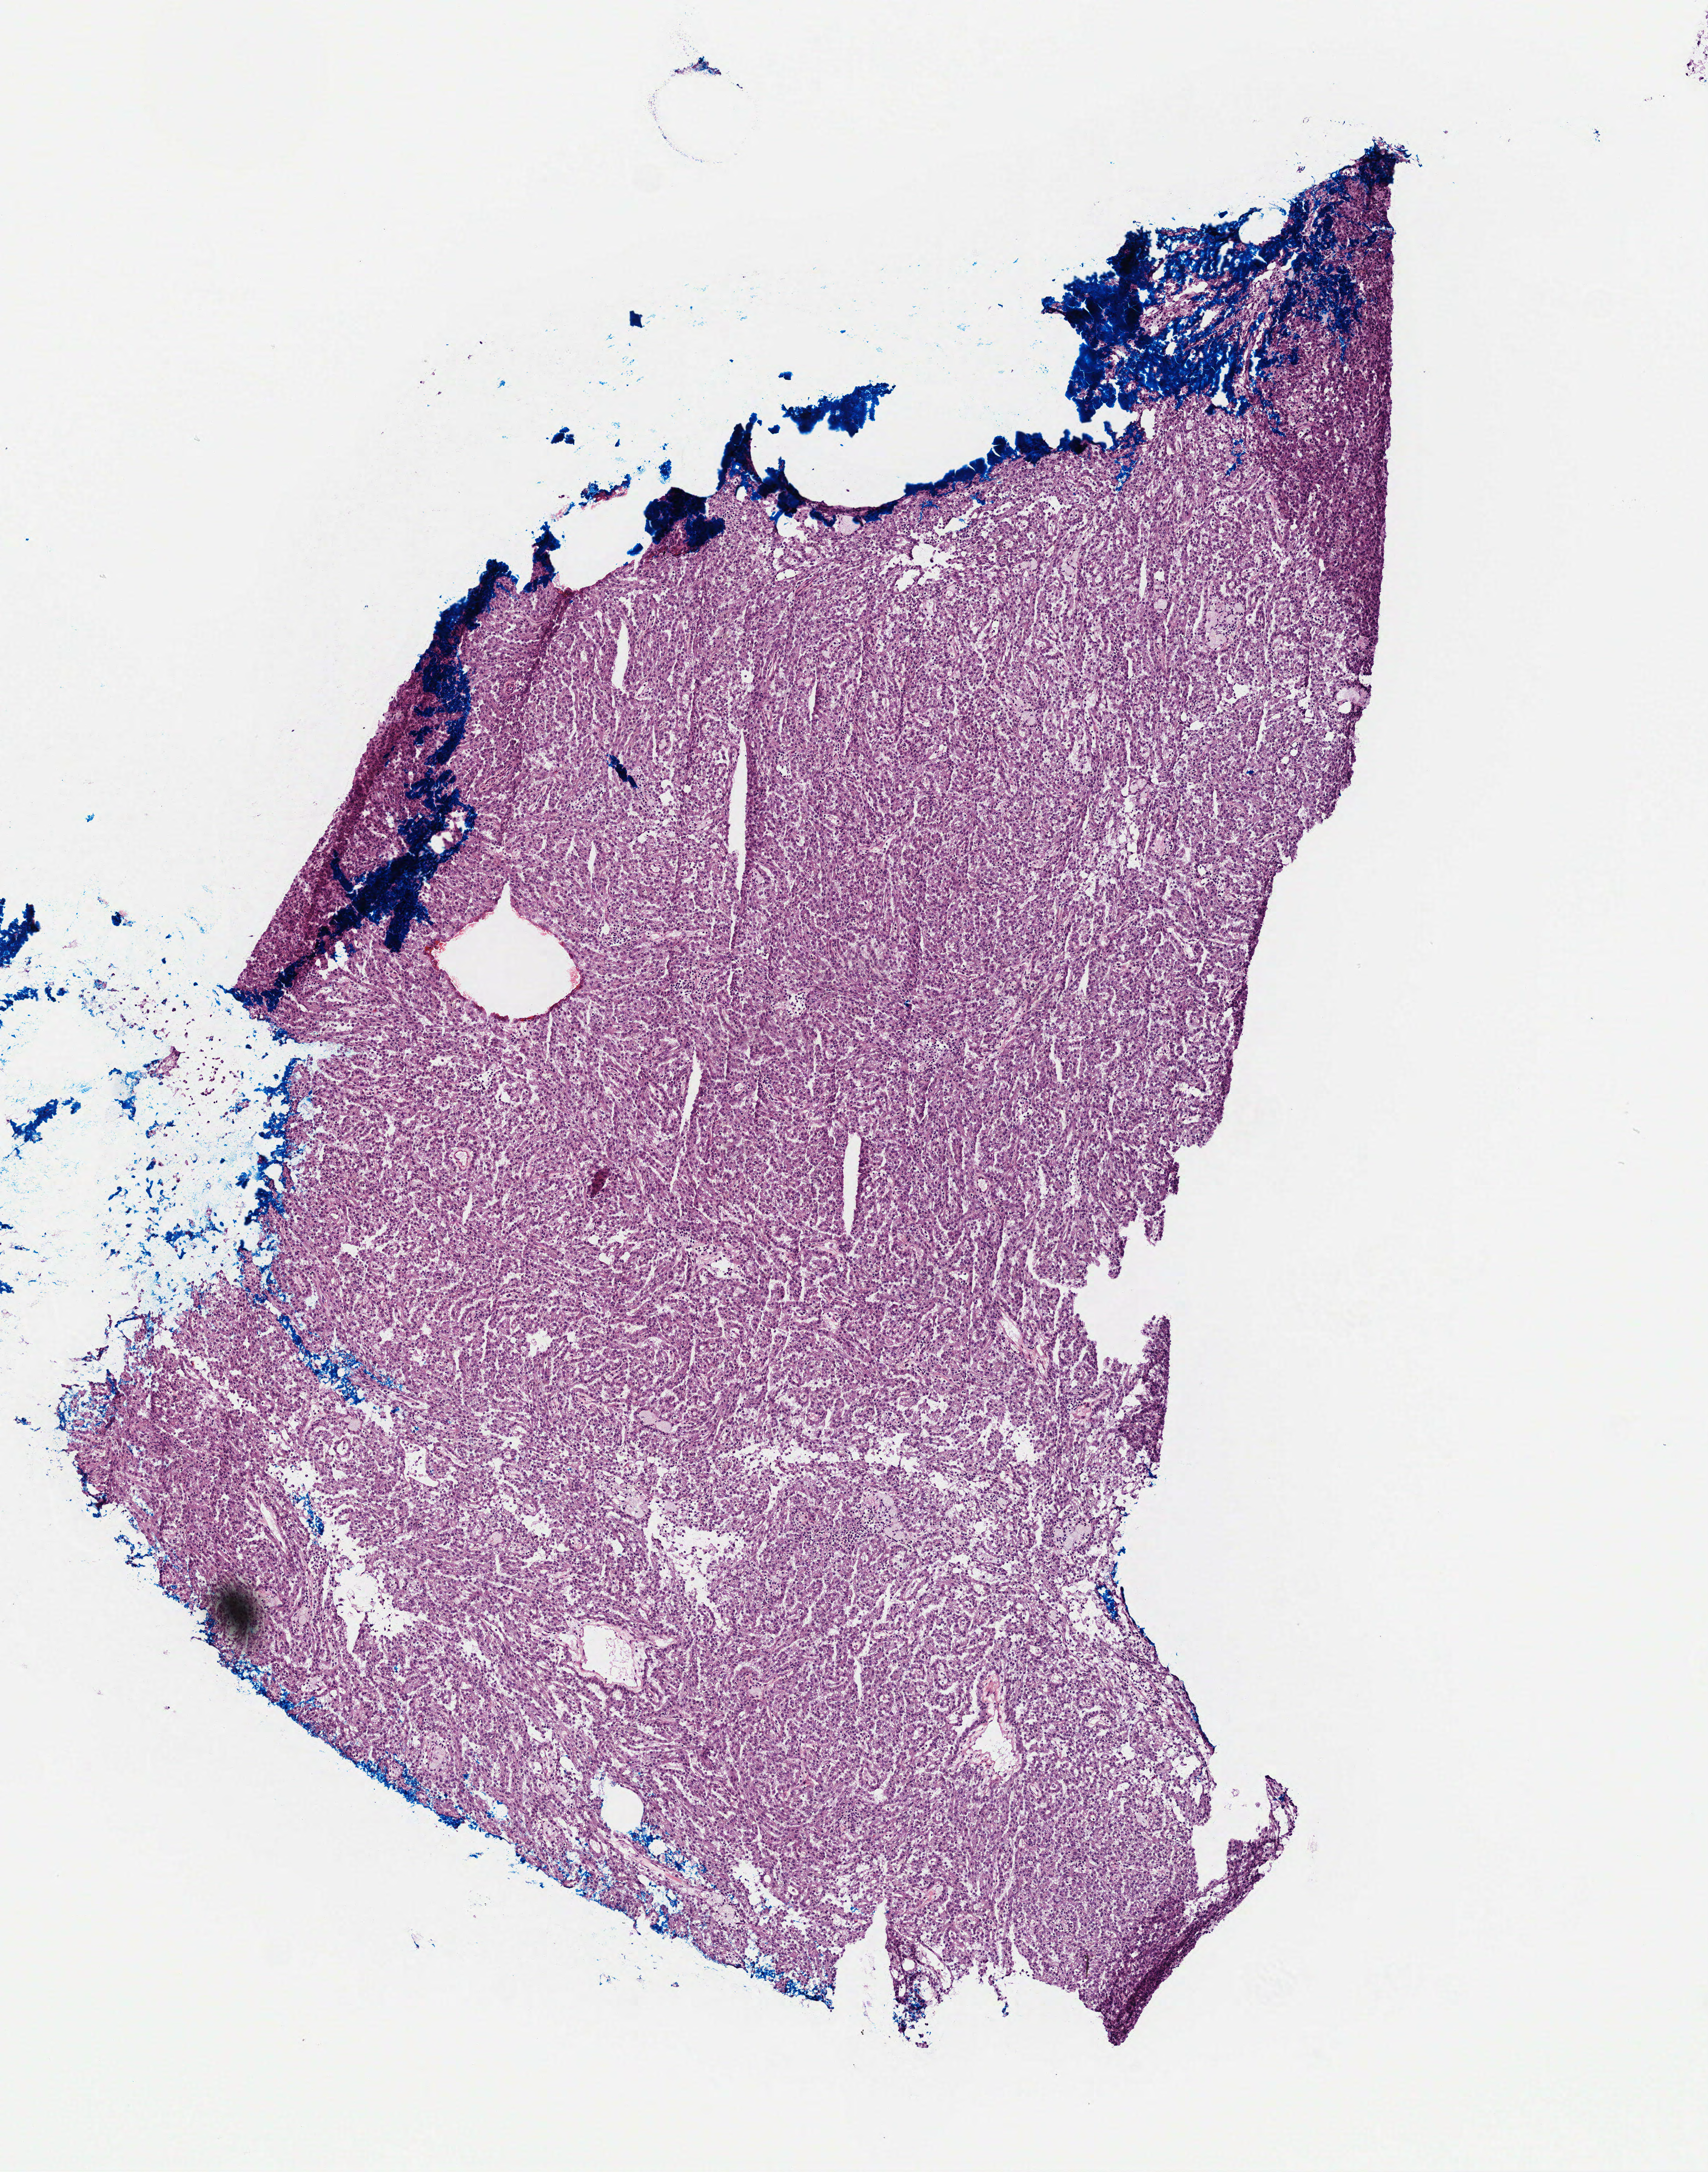
Digitized Hematoxylin and eosin (H&E) stained tissue section (whole slide) — a low-resolution overview of the entire scanned area, about 4.8 x 6.1 mm. Frozen section from the top of the tissue portion. Kidney, primary tumour sample. Male, age 60 years at initial diagnosis. Composition of this section per pathologist review: tumour cells 100%, tumour nuclei 85%.
Histologic diagnosis: Papillary adenocarcinoma, NOS.